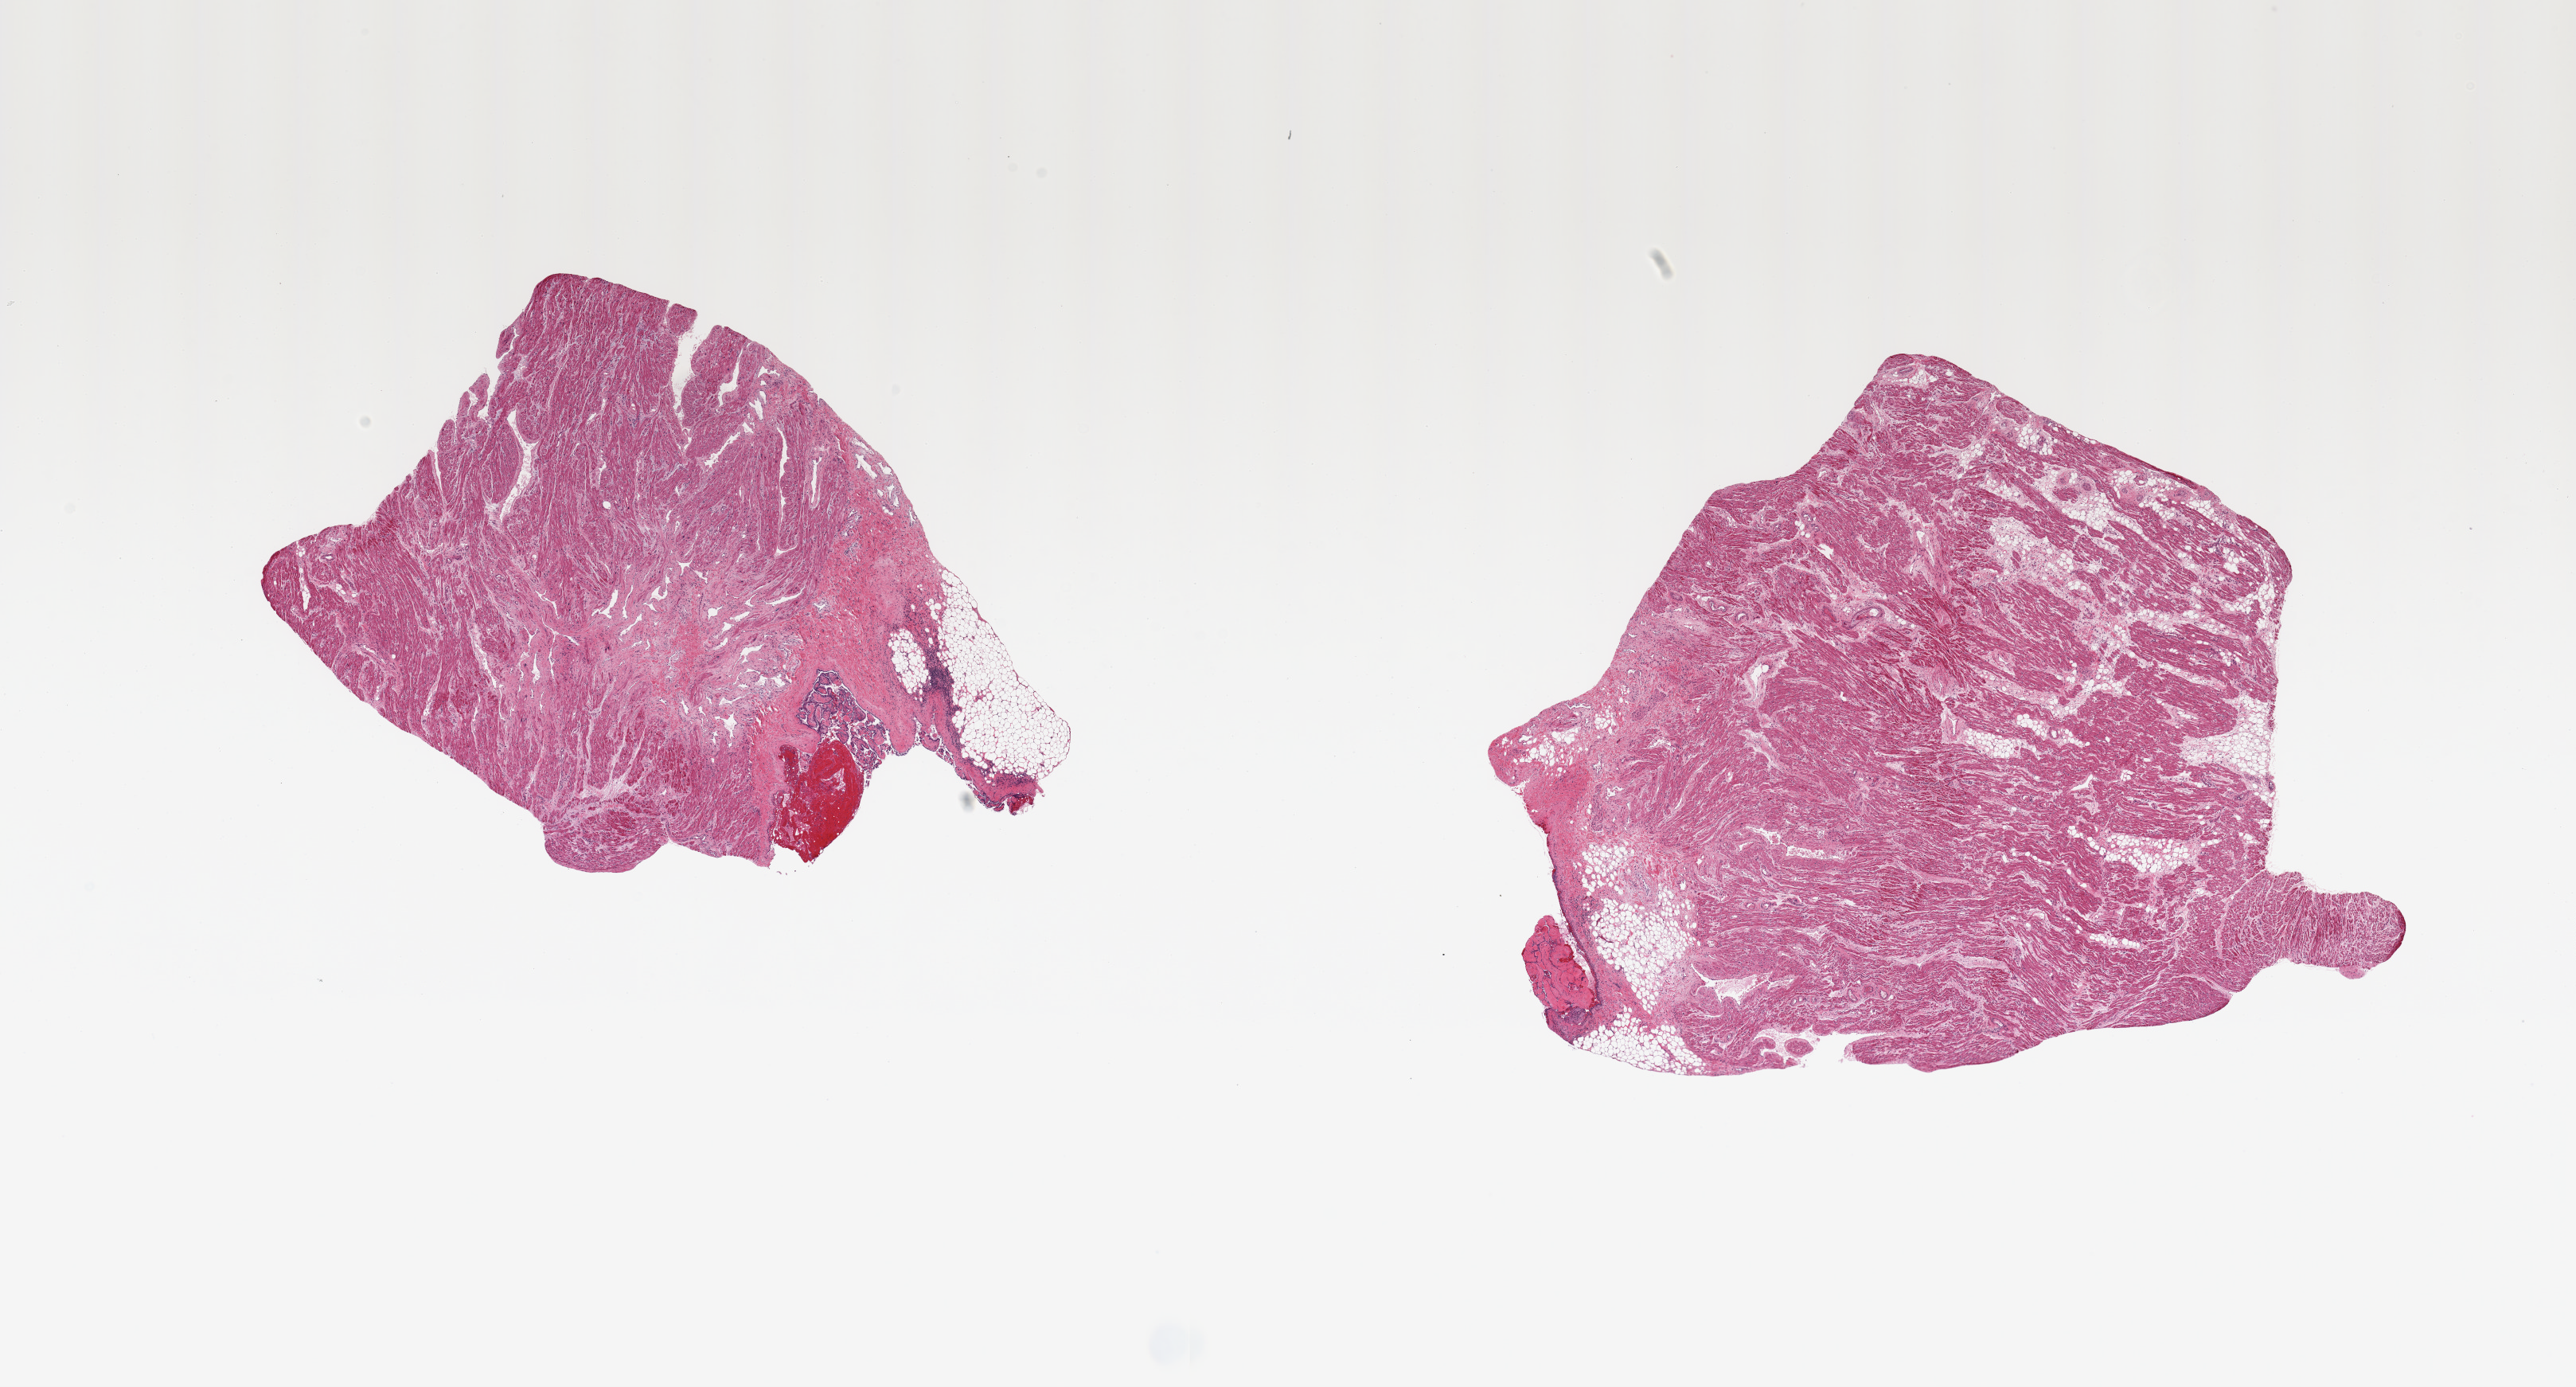
Whole-slide image, haematoxylin and eosin stain, shown as a low-resolution overview of the whole scanned area (about 25.6 x 13.8 mm), PAXgene-fixed paraffin-embedded (PFPE) section, sampled site (target tissue): auricular appendage, tissue donor sample. Male donor.
- reviewer comment on this tissue sample: 2 pieces; 20% fibrofatty content; focal percardial hyperplasia up to 1 mm